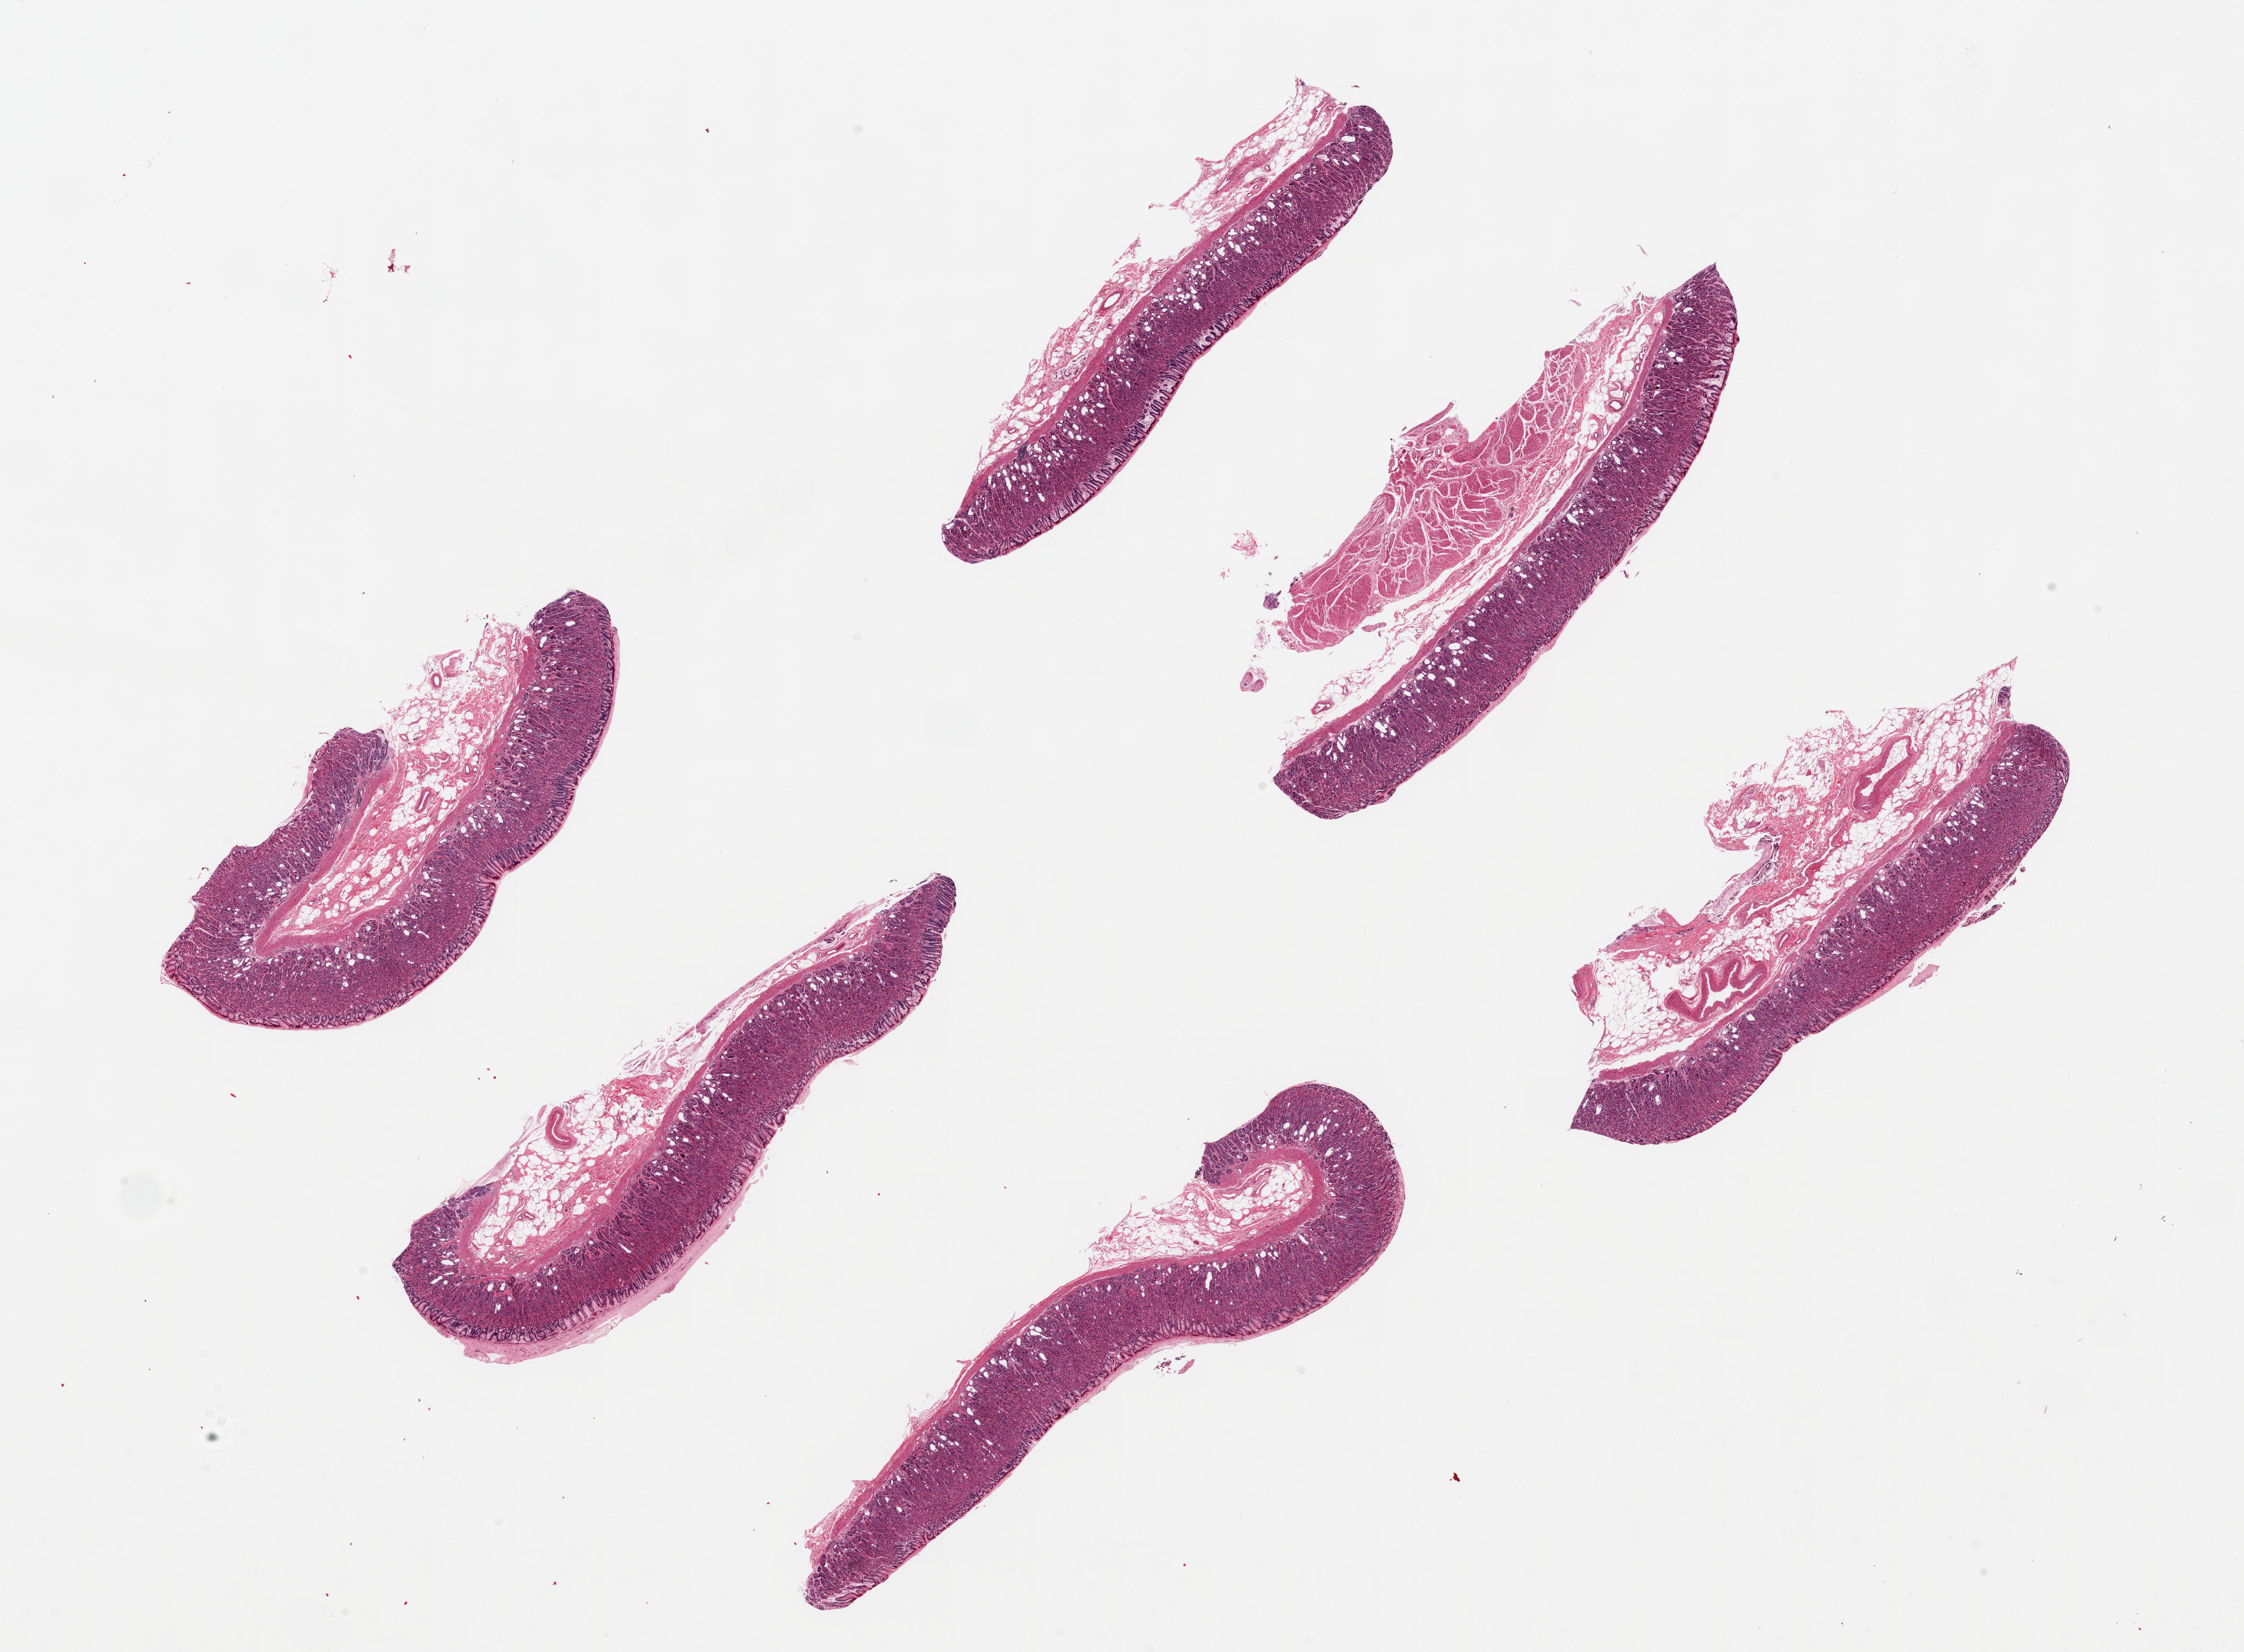
H&E whole-slide image — whole scanned area (about 25.6 x 18.8 mm, acquisition: 20x scan) shown as a low-resolution overview, PAXgene-fixed paraffin-embedded (PFPE) section, section of stomach (target tissue), tissue donor sample. Donor: male.
Review note (as recorded): 6 pieces, 7.5x1.5mm. Mucosa extremely well-preserved, 40-50% of thickness.